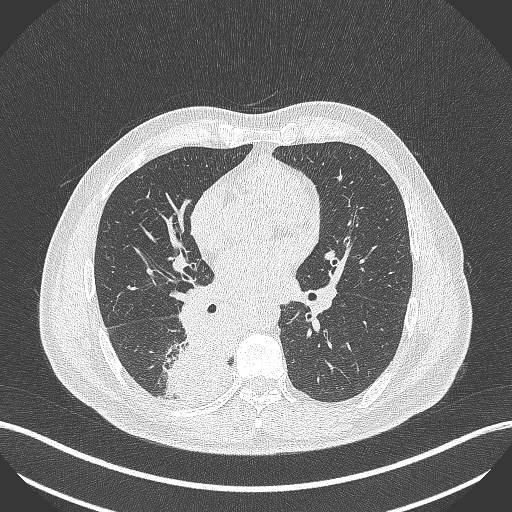
Chest CT, one axial slice; position 235 of 451 along the scan axis; lung window (W 1500 / L -600 HU); 1 mm slice thickness; 512 × 512 image matrix, field of view 400 × 400 mm. Patient: male, 61 years. From the clinical record (not read from this slice): clinical TNM (as recorded): T1 N0 M0; histopathological grade: G3.
Annotated regions visible in this slice (rectangle marked by the reading radiologist):
- lung tumour (recorded histology: small cell carcinoma): box from (x=163, y=314) to (x=232, y=399) px